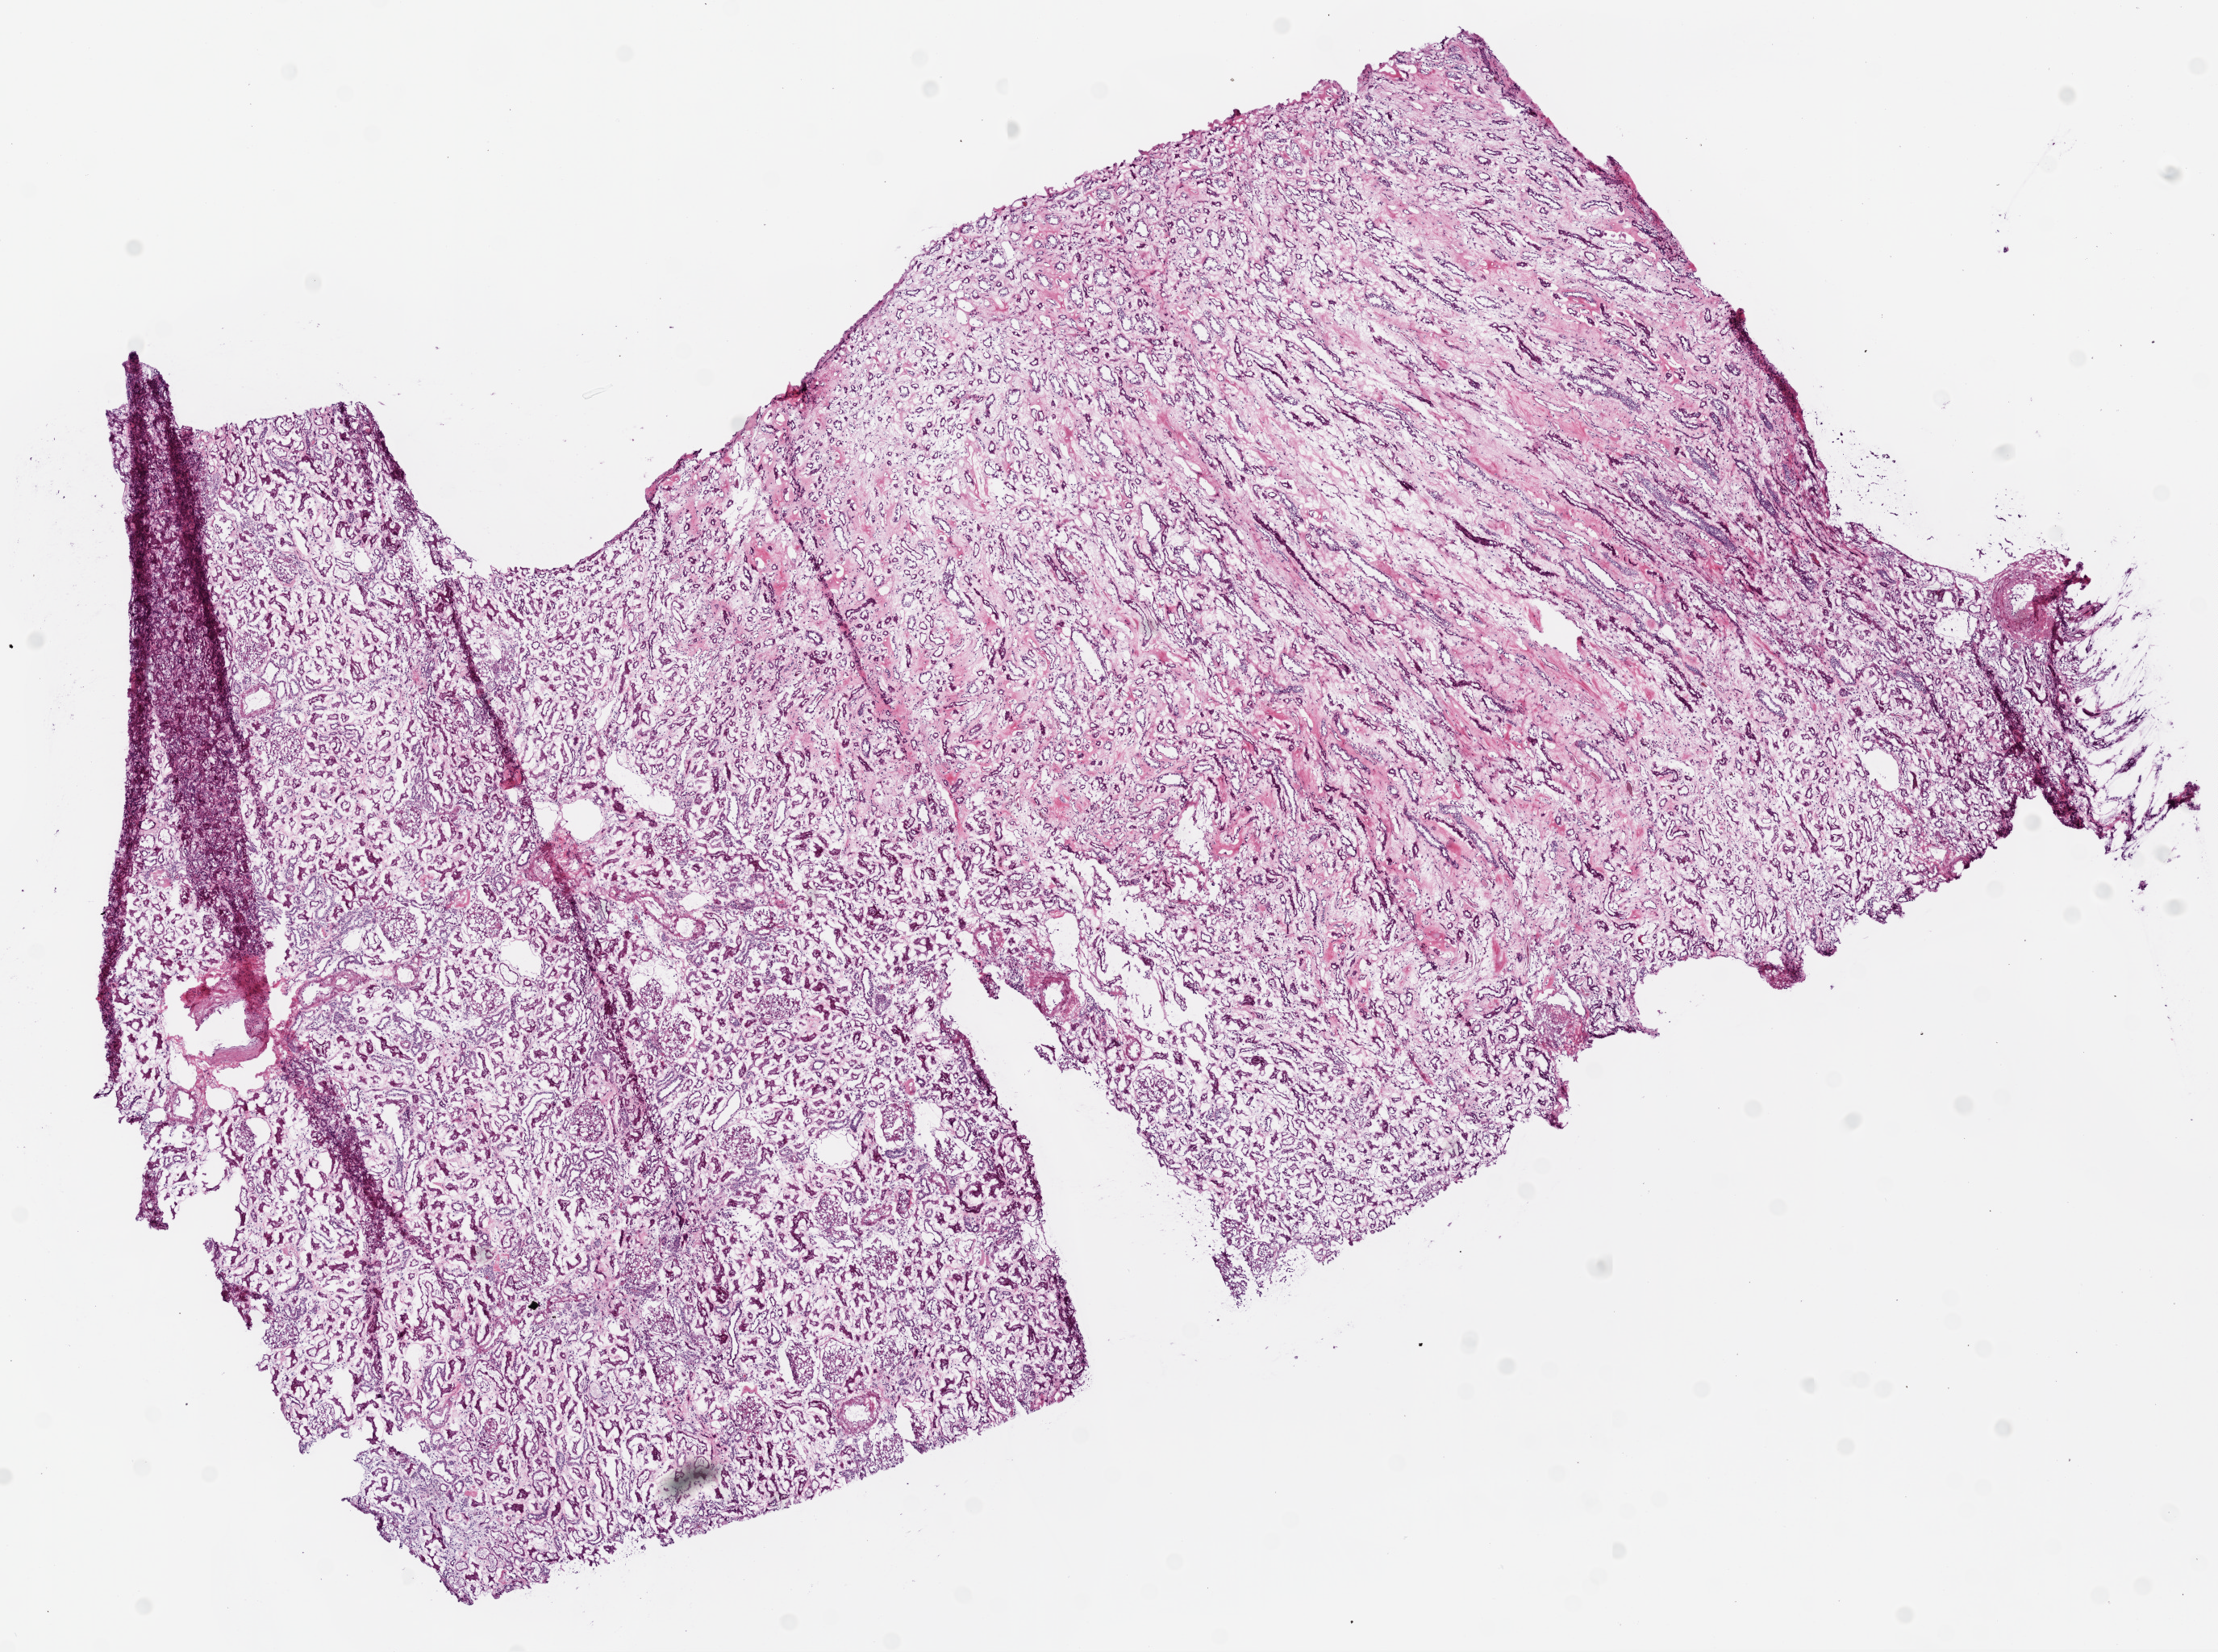
Whole-slide histology image, H&E, shown as a low-resolution overview of the whole scanned area (about 11.0 x 8.2 mm, acquisition: 20x scan); frozen section from the top of the tissue portion; sample: solid tissue normal (non-tumour tissue), kidney. Male patient; age at initial diagnosis 72 years.
• this section: solid tissue normal sample (biorepository sample class)
• patient diagnosis: Clear cell adenocarcinoma, NOS